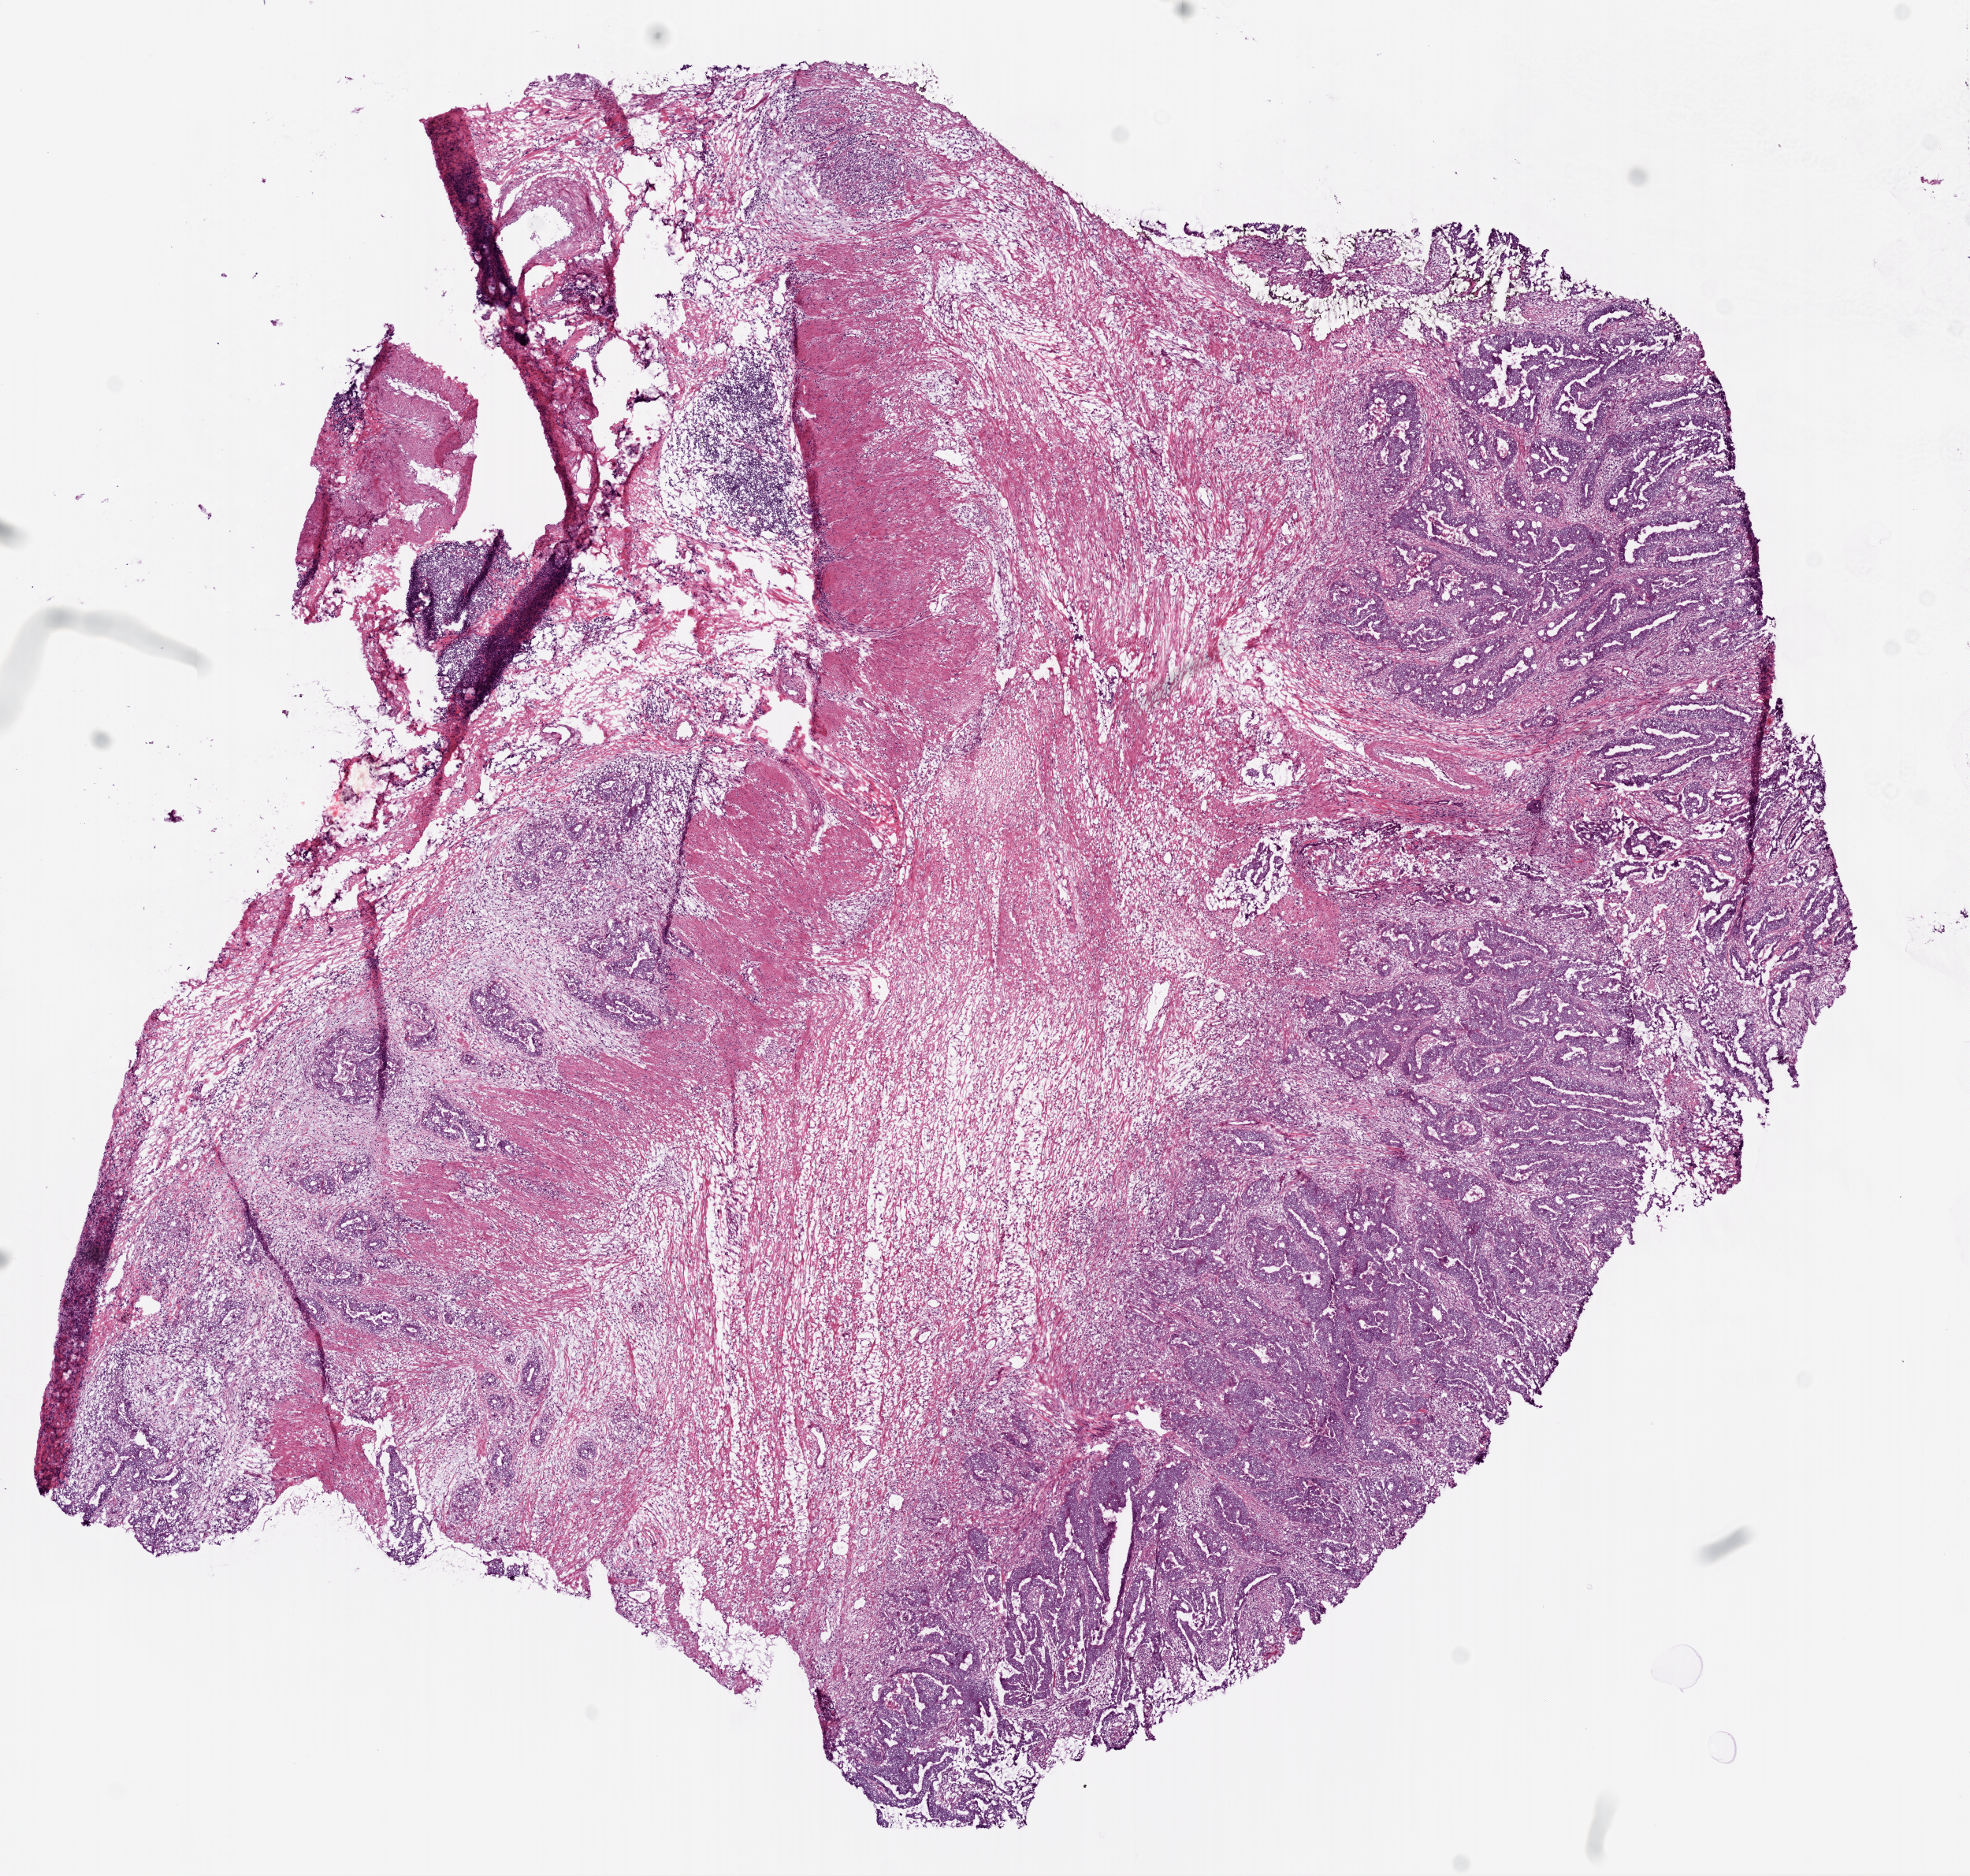
Whole-slide histology image, H&E-stained, whole scanned area (about 10.0 x 9.6 mm, slide scanned at 20x) shown as a low-resolution overview, frozen section from the bottom of the tissue portion, sample: primary tumour, colon. Patient: male, age at initial diagnosis 65 years. Composition of this section per pathologist review: tumour cells 50%, tumour nuclei 60%, normal cells 48%, stromal cells 0%, necrosis 2%. Inflammatory infiltration, as recorded: lymphocyte infiltration 10%, monocyte infiltration 1%, neutrophil infiltration 10%.
* diagnosis: Adenocarcinoma, NOS
* AJCC pathologic stage: IIIB